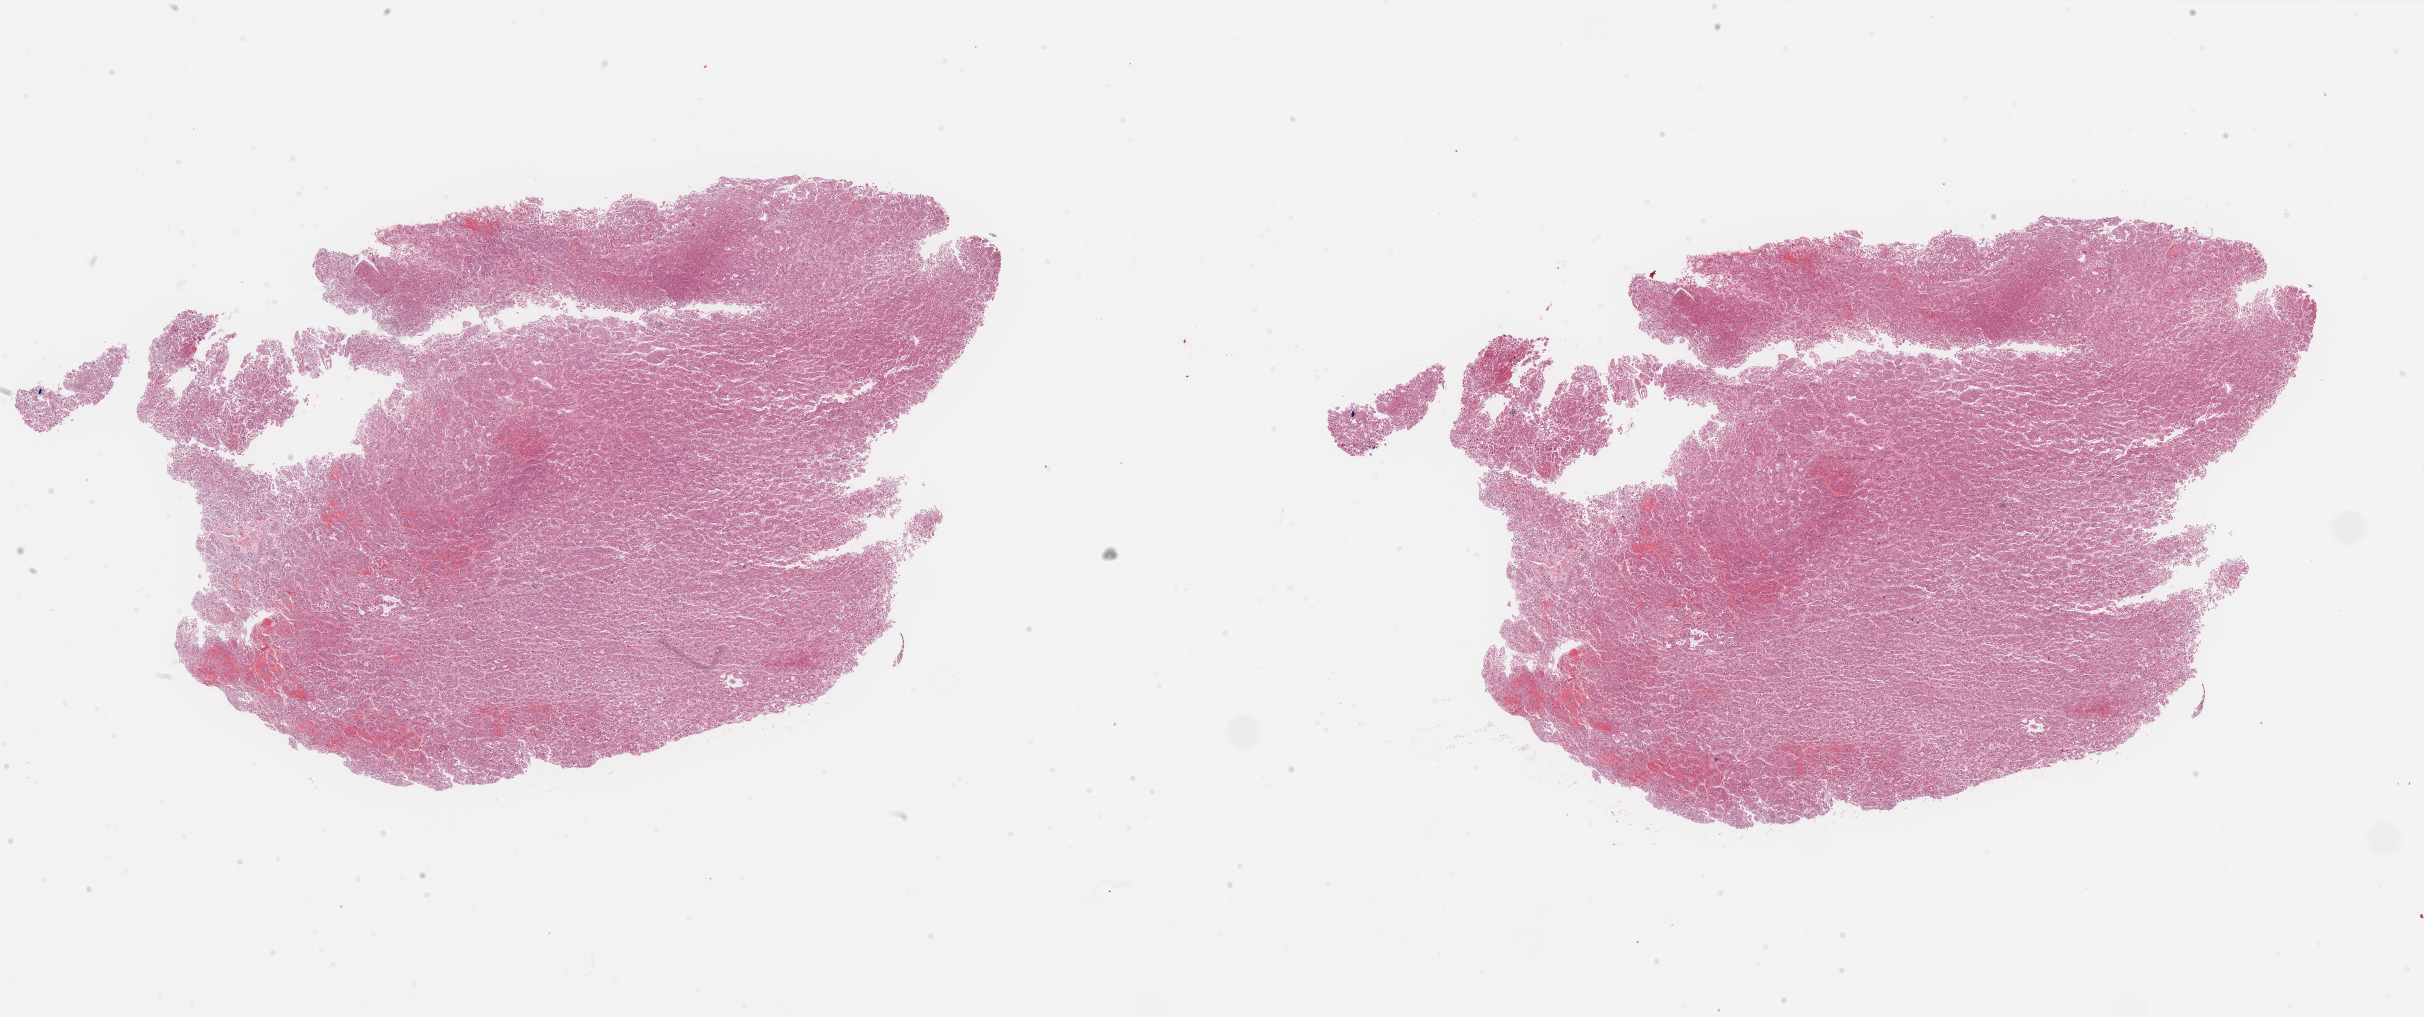
Hematoxylin and eosin (H&E) stained whole-slide image, shown as a low-resolution overview of the whole scanned area (about 38.4 x 16.1 mm, from a 40x scan), FFPE section, primary tumour sample from the kidney. Patient: male, age at initial diagnosis 52 years.
TNM: T1a NX. Pathologic diagnosis: Renal cell carcinoma, chromophobe type. AJCC pathologic stage: I. Laterality: left.